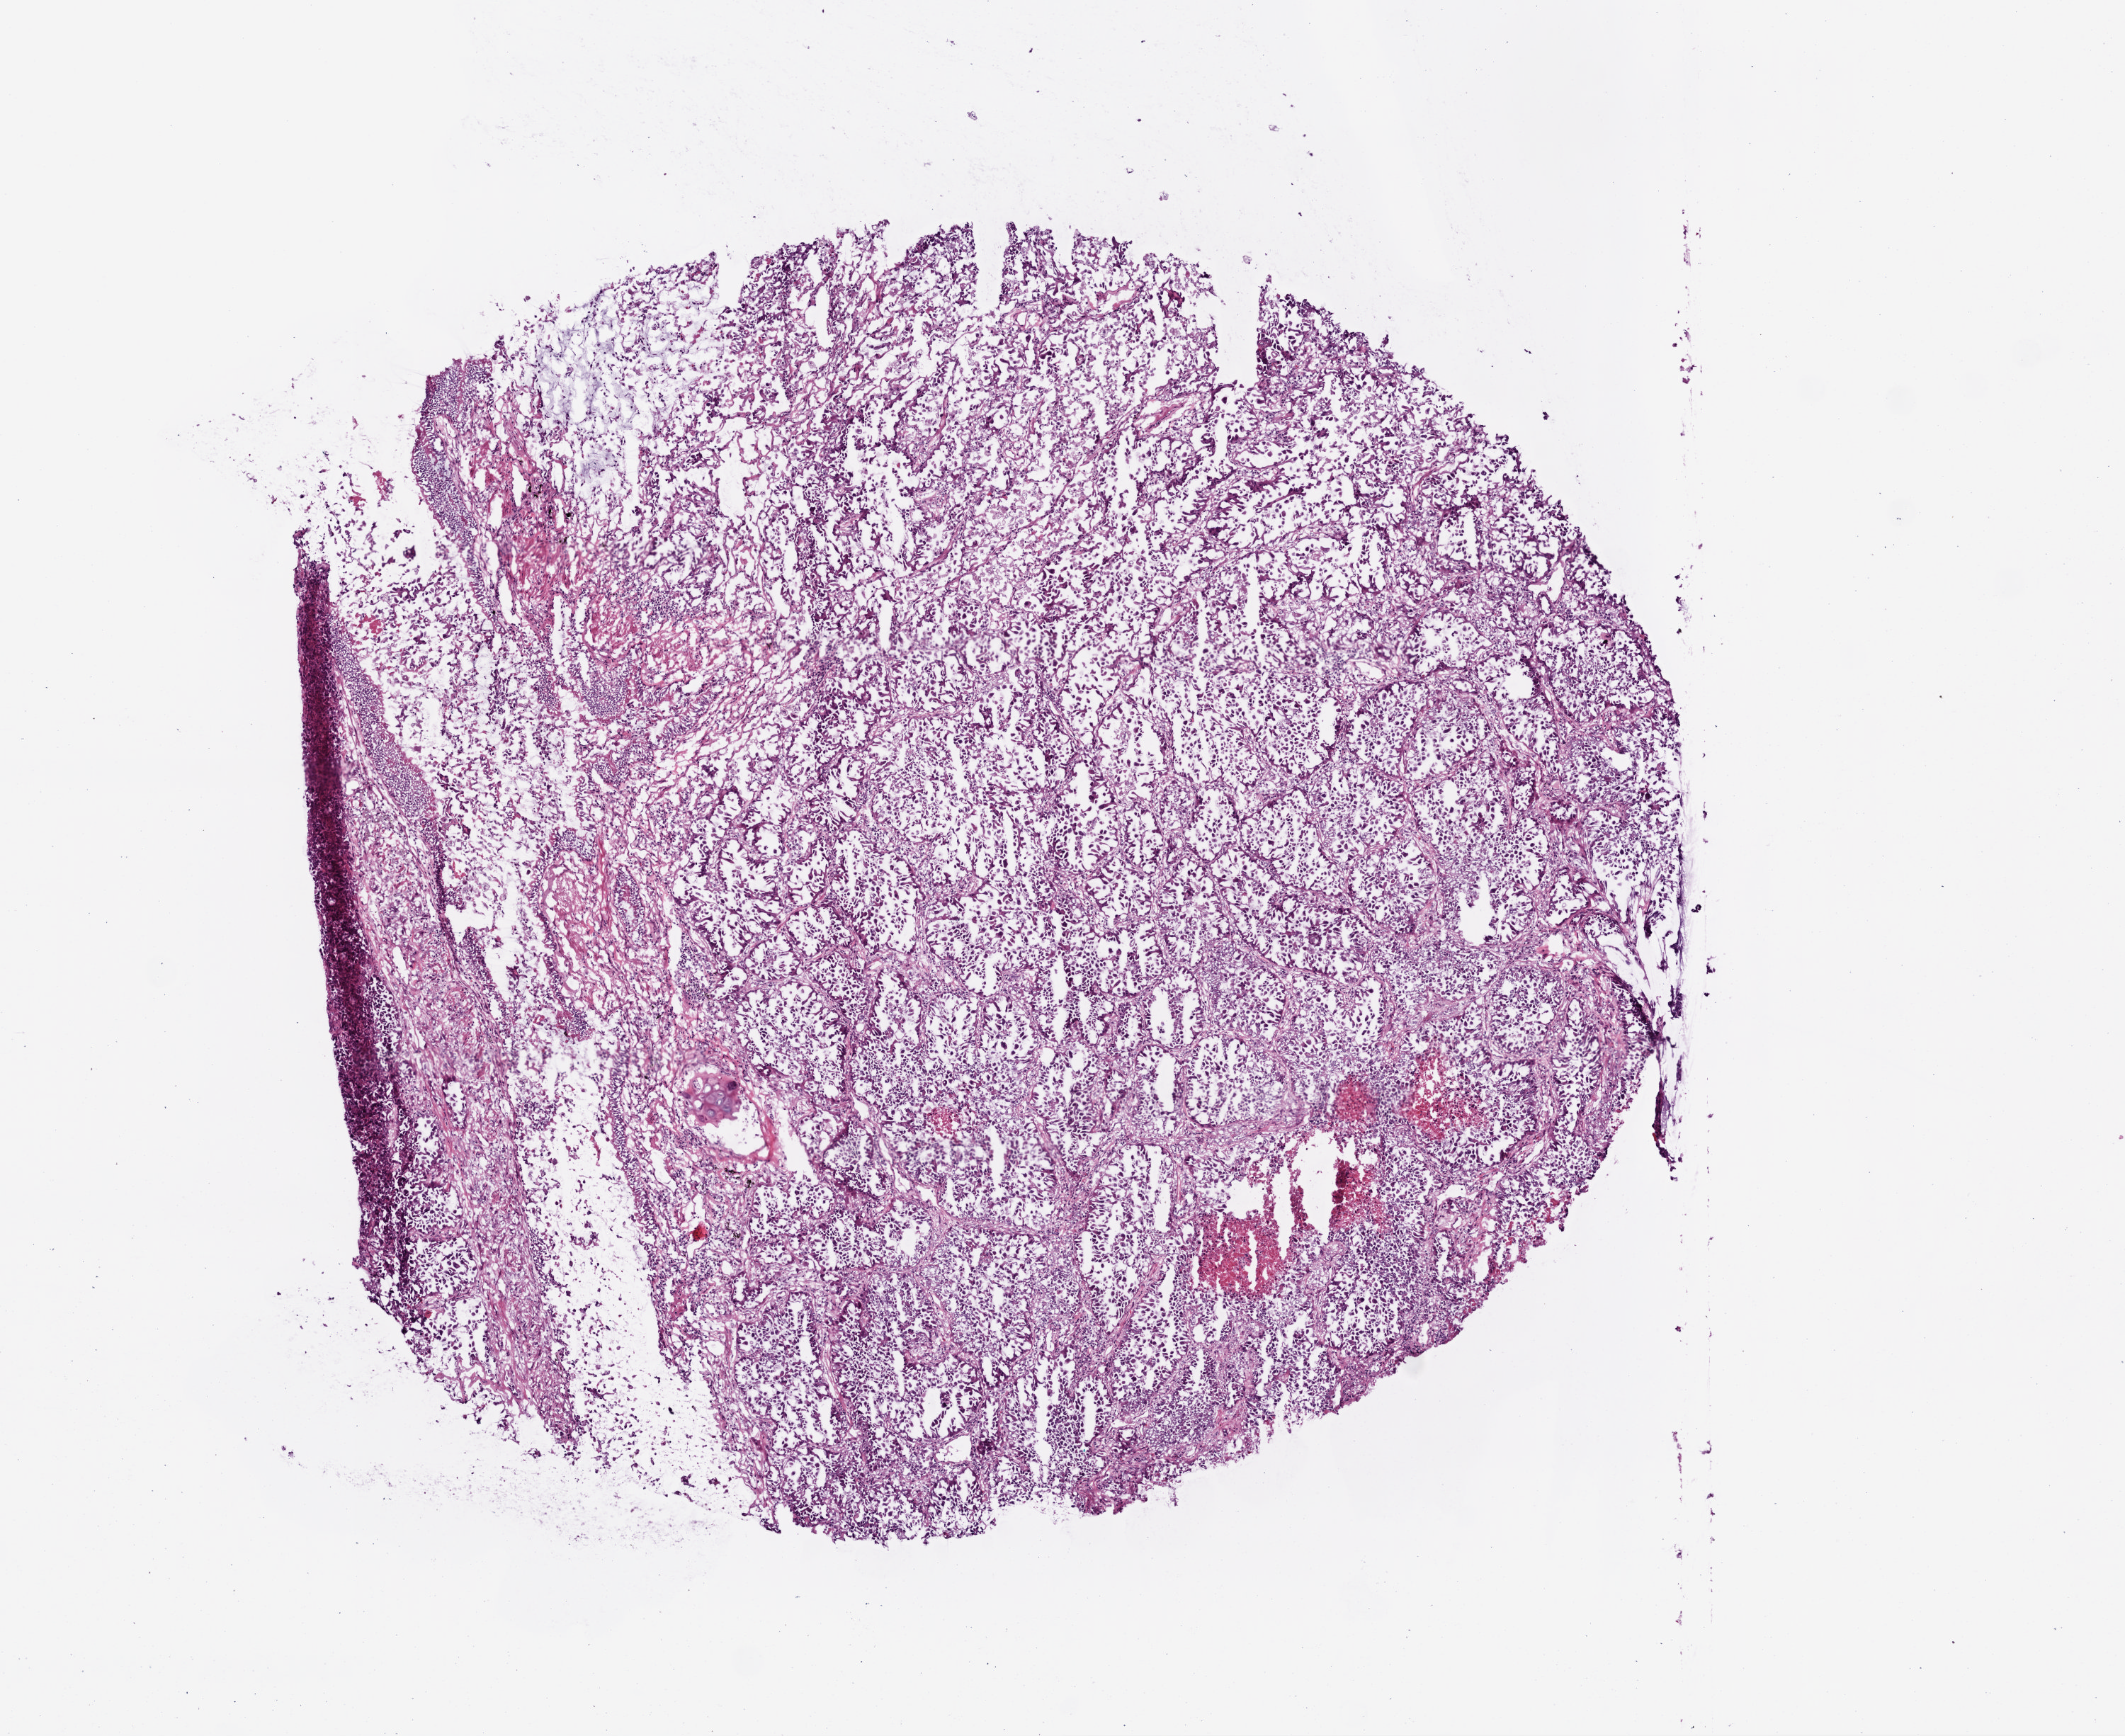
Whole-slide histology image, H&E-stained, shown as a low-resolution overview of the whole scanned area (about 6.0 x 4.9 mm). Frozen section from the top of the tissue portion. Sample: primary tumour, lung. Patient: male, age at initial diagnosis 70 years. Slide review estimates, as recorded: tumour cells 70%, tumour nuclei 80%, normal cells 10%, stromal cells 20%, necrosis 0%.
Pathologic diagnosis: Adenocarcinoma, NOS. TNM: T2 N2 M1. AJCC pathologic stage: IV.